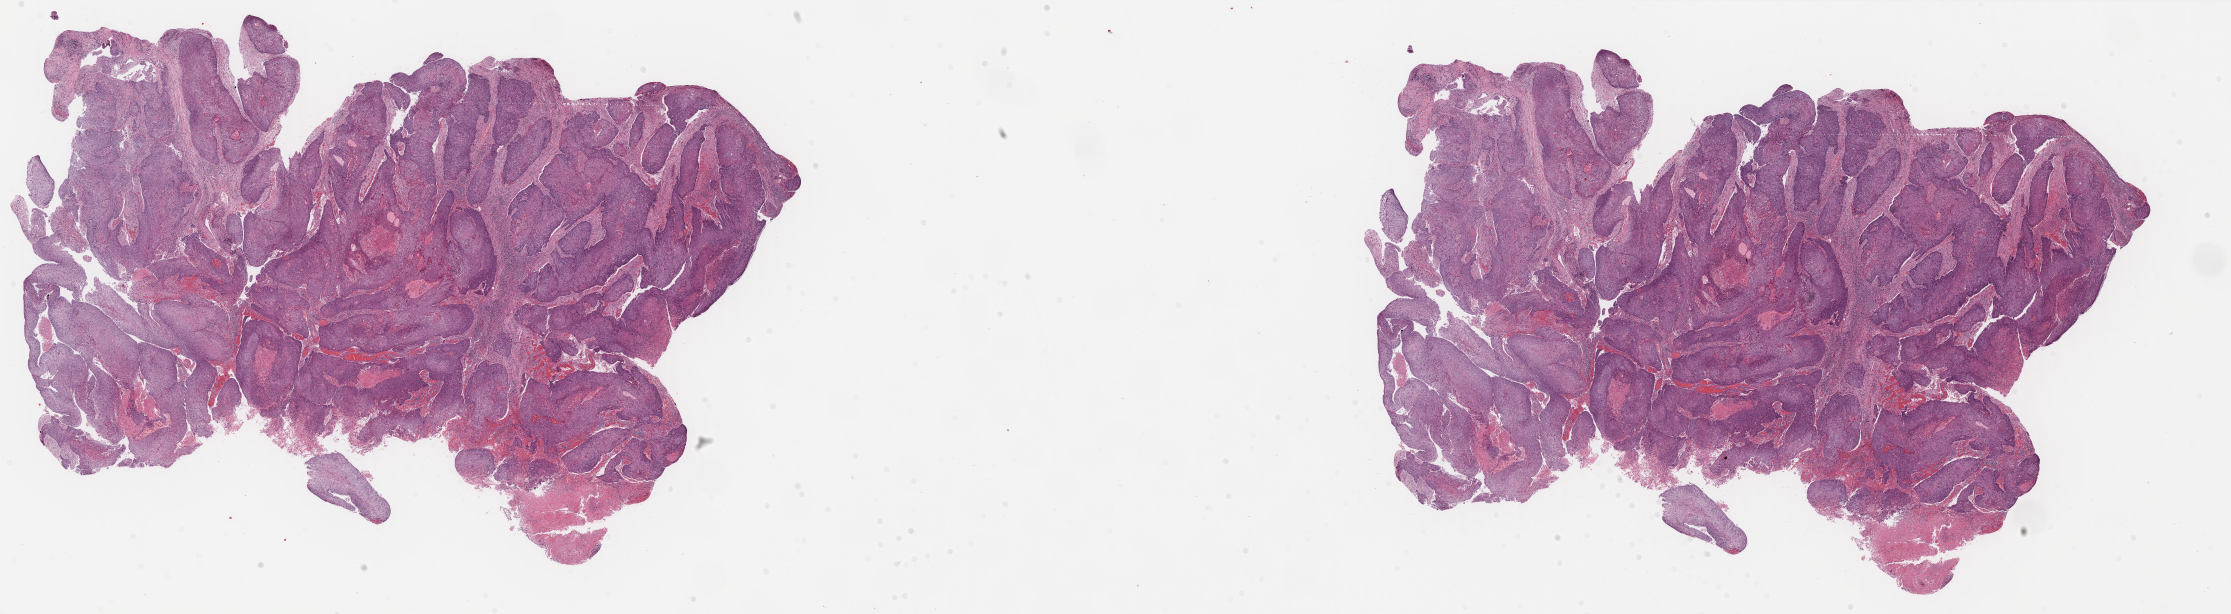
Digitized Hematoxylin and eosin (H&E) stained tissue section (whole slide) — a low-resolution overview of the entire scanned area, about 35.3 x 9.7 mm (slide scanned at 40x), formalin-fixed paraffin-embedded (FFPE) diagnostic section, primary tumour sample from the bladder. Male, age 75 years at initial diagnosis. Histologic grade: high grade.
Lymph nodes positive (case pathology): 0 of 8 examined. AJCC pathologic stage: III (7th edition). Histologic diagnosis: Transitional cell carcinoma.